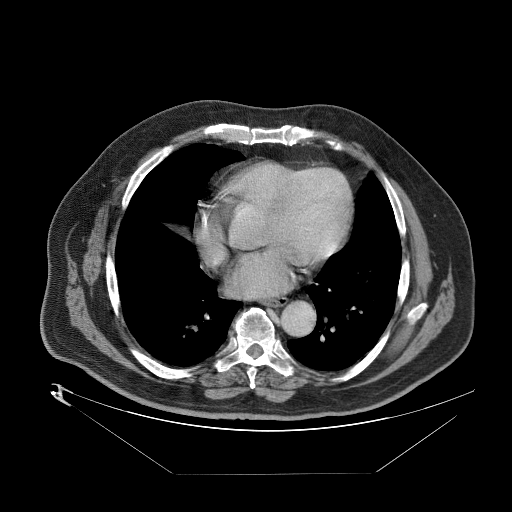
Contrast-enhanced abdominal CT (liver protocol), one axial slice. Slice 88 of 89 in the series (ordered by position). Reconstruction kernel STANDARD. 140 kVp. One of 2 acquisitions stored at this slice position. Soft-tissue window (W 400 / L 40 HU). 2.5 mm slice thickness. 512 × 512 image matrix. From the clinical record (not read from this slice): diagnosis: hepatocellular carcinoma (patient treated with transarterial chemoembolisation; whether this scan precedes or follows treatment is not stated here); TNM stage (as recorded): Stage-II; Child-Pugh class: B.
Outlined on this slice (semi-automatically segmented with operator editing):
- abdominal aorta: bounding box (x1, y1, x2, y2) in pixels: (280, 302, 313, 336)